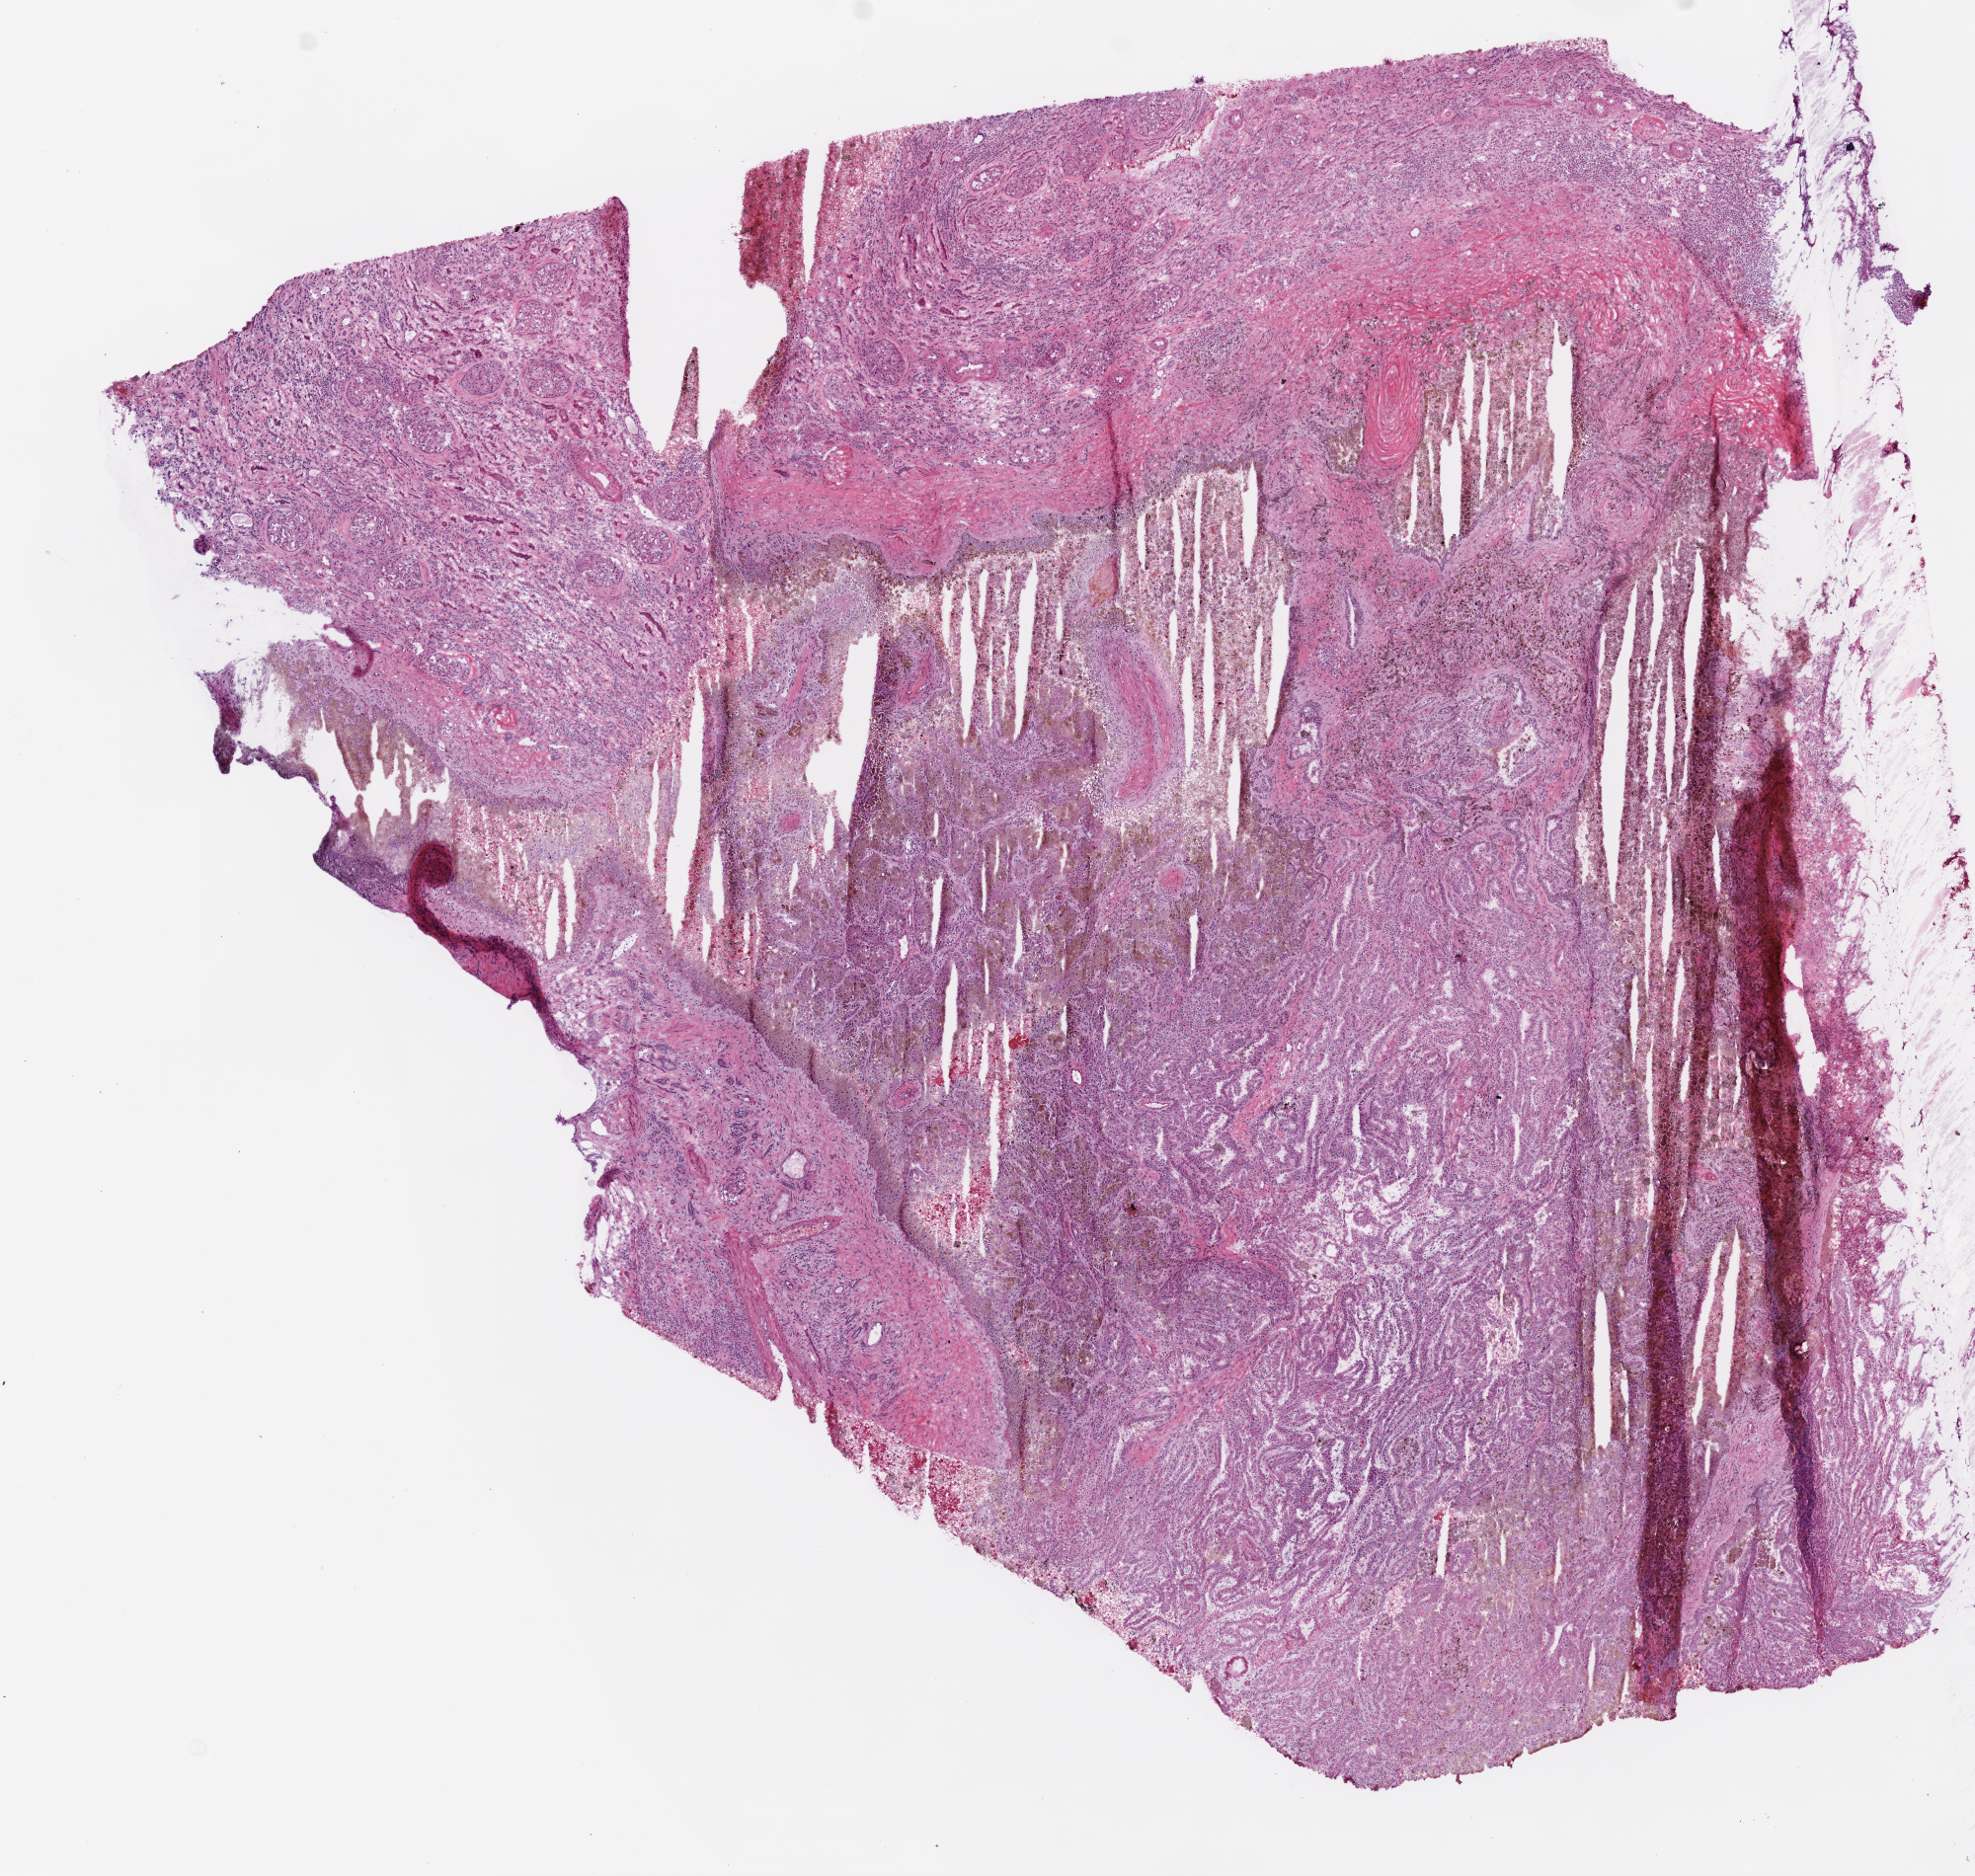
H&E whole-slide image — a low-resolution overview of the entire scanned area, about 8.0 x 7.6 mm (acquisition: 20x scan), frozen section from the top of the tissue portion, primary tumour sample from the kidney. Male patient; age at initial diagnosis 56 years. Pathologist review of this section (percent, as recorded): tumour cells 50%, tumour nuclei 75%, normal cells 20%, stromal cells 15%, necrosis 15%.
Pathologic diagnosis: Papillary adenocarcinoma, NOS. AJCC pathologic stage: I.